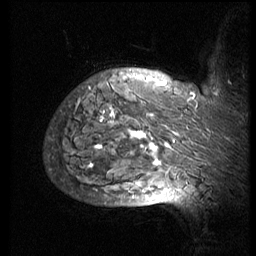
Breast MRI (dynamic contrast-enhanced), one sagittal slice. Slice 61 of 74 in the series (ordered by position). 3 images stored at this slice position (order not interpretable as contrast timing). 1.5 T. TE 4.2 ms, TR 8.9 ms. 256 × 256 image matrix, field of view 200 × 200 mm. Patient: female, 57 years. From the clinical record (not read from this slice): setting: breast cancer imaged before/during neoadjuvant chemotherapy; receptor status: HER2-positive.
Structures marked on this image (semi-automatic segmentation, software-assisted and operator-edited):
- analysis volume of interest (the breast-tissue region the enhancement analysis was run in; not a lesion): bounding box (x1, y1, x2, y2) in pixels: (51, 67, 248, 173)
- tumour enhancement mask (voxels above the 140 % enhancement threshold inside the analysis volume of interest): (89, 83, 170, 168)